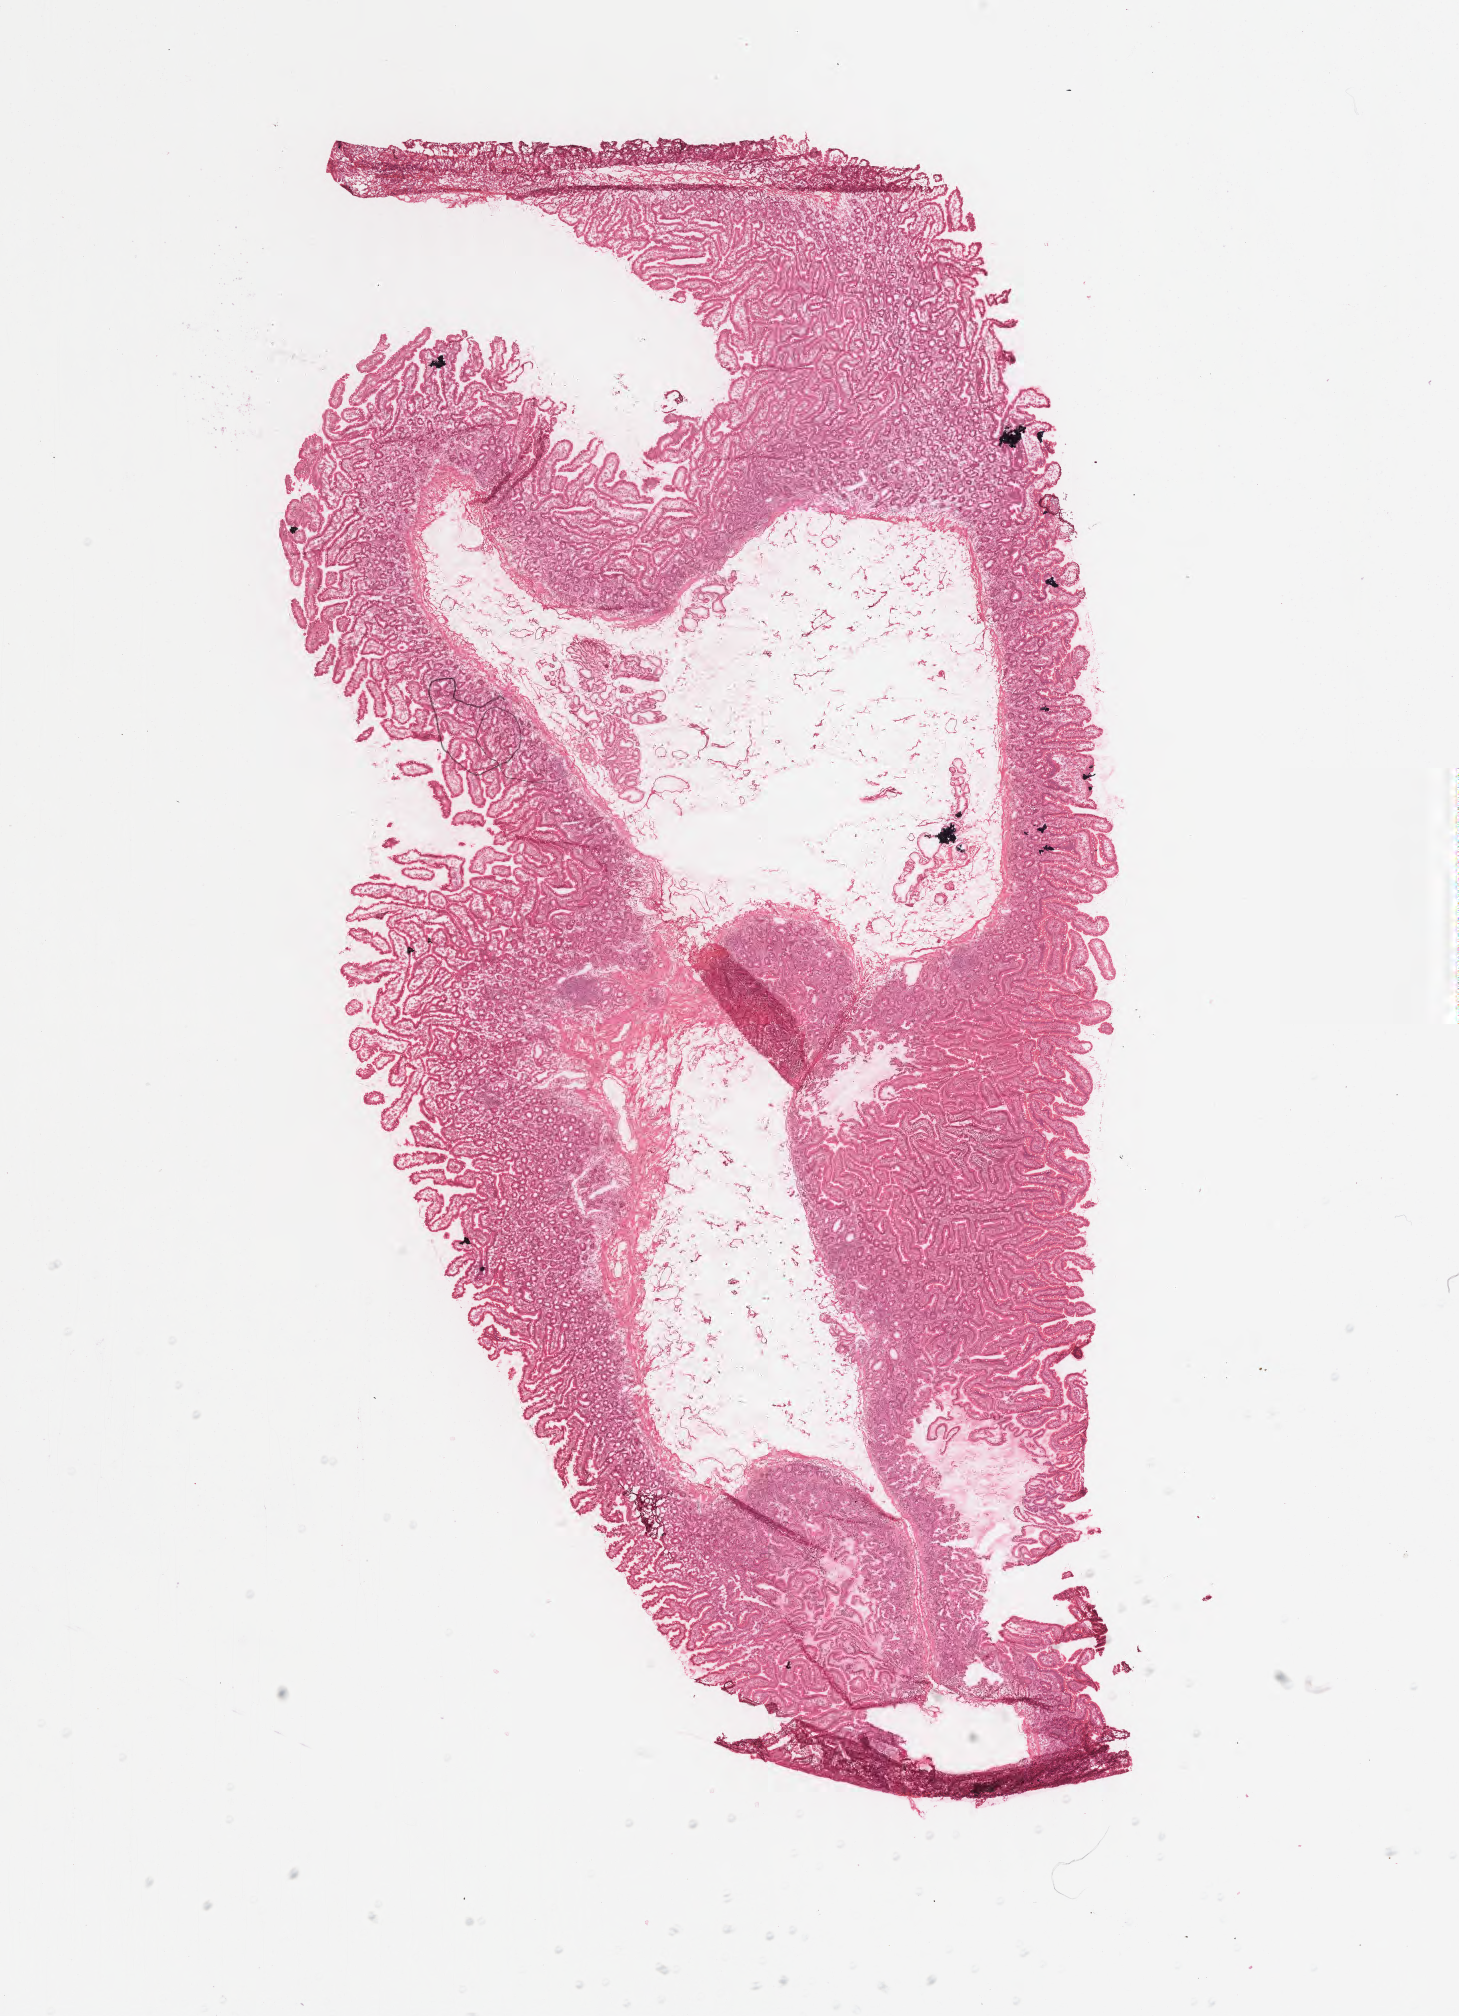
Whole-slide image, H&E stain, low-resolution overview of the scanned area, about 11.5 x 15.9 mm; frozen section; specimen: normal-tissue sample (non-tumor) from a patient with infiltrating duct carcinoma, NOS; site: head of pancreas. Patient: female, age at initial diagnosis 70 years. Composition of this section per pathologist review: tumor cells 0%, tumor nuclei 0%, stromal cells 35%, necrosis 0%, normal cells 65%. Infiltration values recorded for this section: lymphocyte infiltration 10%, monocyte infiltration 6%, neutrophil infiltration 8%.
- this section: non-tumor tissue sample; the patient's diagnosis is given above
- section: top of the tissue portion